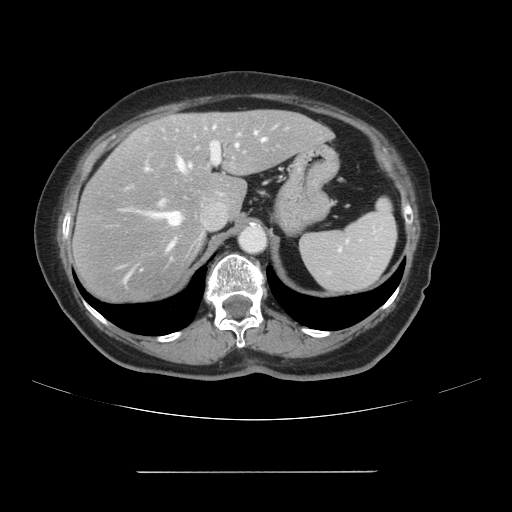
Contrast-enhanced abdominal CT, one axial slice. Slice 73 of 111 in the series (ordered by position). Intravenous contrast given. Soft-tissue window (W 400 / L 40 HU). 2.5 mm slice thickness. 512 × 512 image matrix. Female patient, age 74 years. Case-level facts recorded for this patient, not image findings: diagnosis: colorectal cancer liver metastases, imaged before liver resection; multiple liver metastases: yes; largest metastasis: 1.1 cm.
Structures marked on this image (expert manual segmentation):
- hepatic veins: bounding box (x1, y1, x2, y2) in pixels: (118, 131, 267, 285)
- liver: (74, 111, 332, 304)
- planned liver remnant (the part of the liver to remain after resection): (154, 111, 331, 216)
- portal vein (with intrahepatic branches): (146, 127, 220, 205)